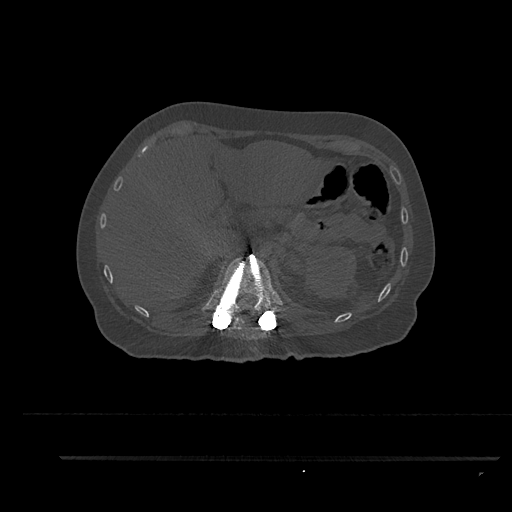
CT including the spine, one axial slice. Slice 277 of 797 in the series (ordered by position). 120 kVp. Bone window (W 1800 / L 400 HU). 0.5 mm slice thickness. 512 × 512 image matrix, field of view 408 × 408 mm. Patient: female, 44 years. Case-level facts recorded for this patient, not image findings: primary cancer: renal; vertebrae with lytic lesions (as recorded): L1.
Annotated regions visible in this slice (semi-automatically segmented with operator editing):
- T11 vertebra: bounding box (x1, y1, x2, y2) in pixels: (233, 317, 253, 341)
- T12 vertebra: (213, 256, 282, 319)